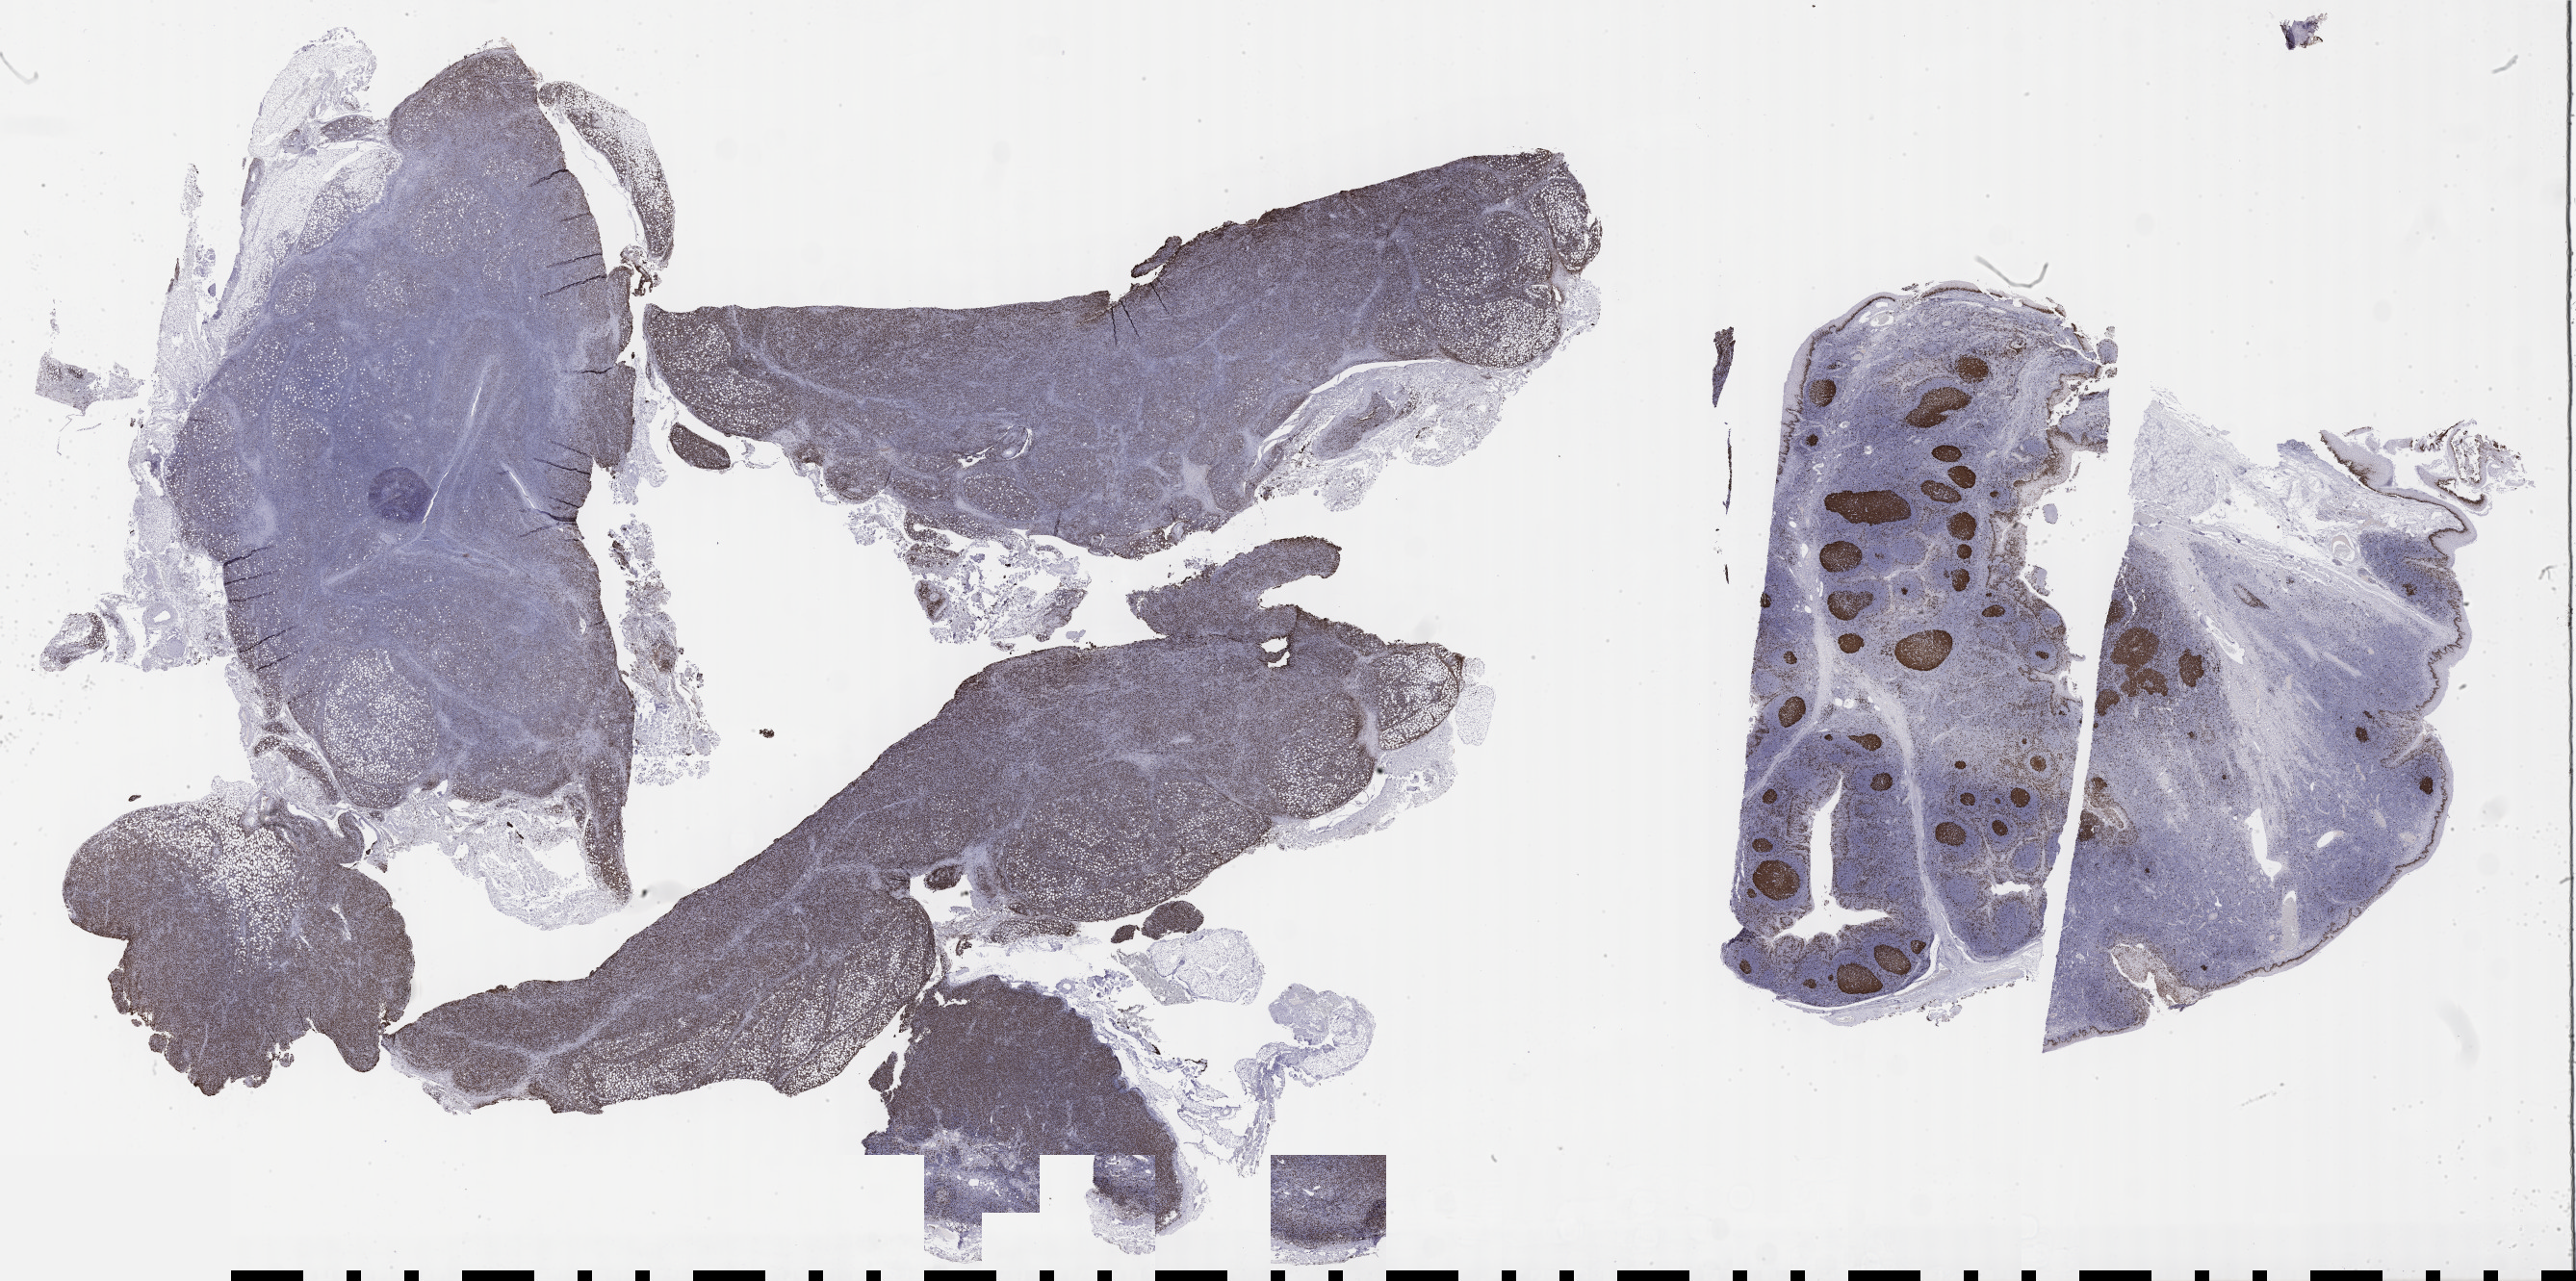
Immunohistochemistry (IHC) whole-slide image stained for Ki-67, shown as a low-resolution overview of the whole scanned area (about 43.3 x 21.5 mm), tumor tissue, anatomic site: lymph node. Patient: male, age 68 years.
Diagnosis: Diffuse large B-cell lymphoma, NOS.